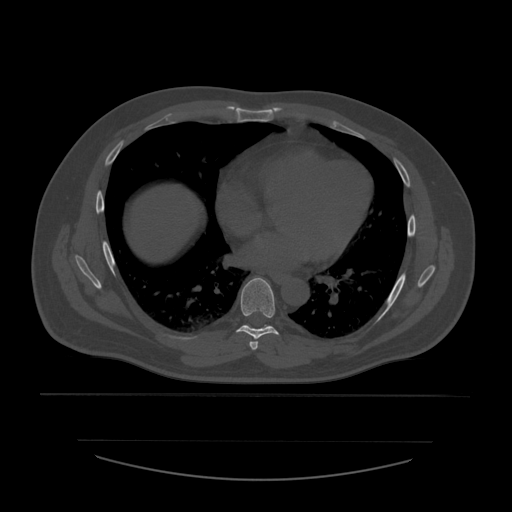
CT including the spine, one axial slice; position 358 of 532 along the scan axis; reconstruction kernel STANDARD; bone window (W 1800 / L 400 HU); 512 × 512 image matrix, field of view 441 × 441 mm. Patient age 44 years. Case-level facts recorded for this patient, not image findings: primary cancer: soft tissue sarcoma.
Structures marked on this image (semi-automatically segmented with operator editing):
- T6 vertebra: bounding box <249,342,258,350> (left, top, right, bottom; pixels)
- T7 vertebra: <237,278,279,340>